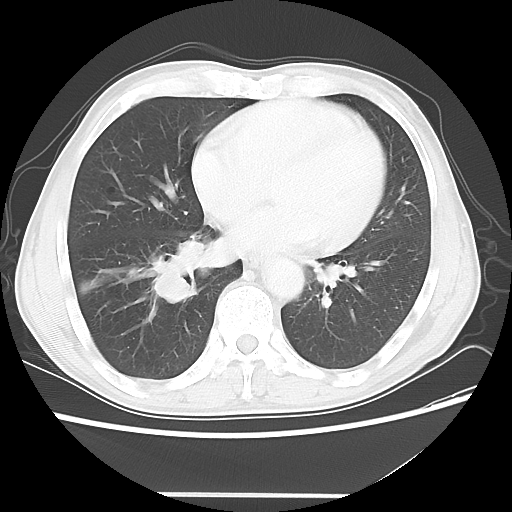
Chest CT, one axial slice; position 21 of 56 along the scan axis; reconstruction kernel LUNG; 120 kVp; lung window (W 1500 / L -600 HU); 5 mm slice thickness; 512 × 512 image matrix, field of view 344 × 344 mm. Male patient, age 65 years. Case-level facts recorded for this patient, not image findings: clinical TNM (as recorded): T1c N3 M0.
Outlined on this slice (rectangle marked by the reading radiologist):
- lung tumour (recorded histology: small cell carcinoma): box from (x=142, y=228) to (x=234, y=308) px